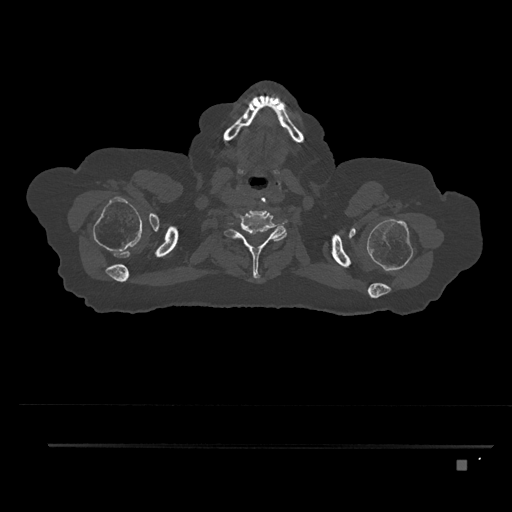
CT including the spine, one axial slice. Slice 734 of 797 in the series (ordered by position). 120 kVp. Bone window (W 1800 / L 400 HU). 0.5 mm slice thickness. 512 × 512 image matrix, field of view 437 × 437 mm. Female patient, age 76 years. From the clinical record (not read from this slice): primary cancer: lung.
Structures marked on this image (semi-automatic segmentation, software-assisted and operator-edited):
- T1 vertebra: bounding box (x1, y1, x2, y2) in pixels: (244, 243, 252, 253)